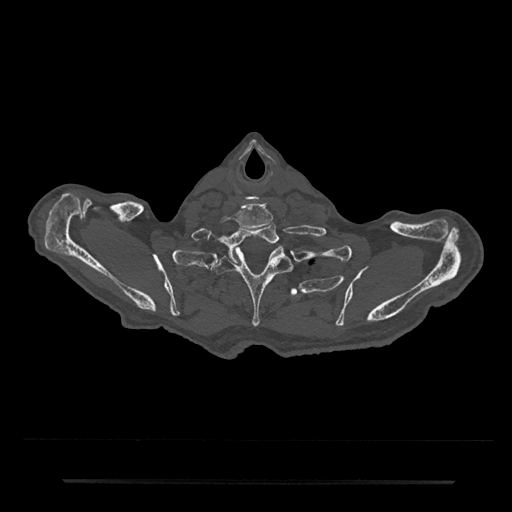
CT including the spine, one axial slice. Slice 706 of 797 in the series (ordered by position). 120 kVp. Bone window (W 1800 / L 400 HU). 512 × 512 image matrix, field of view 427 × 427 mm. Male patient, age 74 years. Case-level facts recorded for this patient, not image findings: primary cancer: prostate.
Annotated regions visible in this slice (semi-automatic segmentation, software-assisted and operator-edited):
- T1 vertebra: box from (x=221, y=222) to (x=279, y=265) px
- T2 vertebra: (x=211, y=248)–(x=292, y=328)
- T3 vertebra: (x=290, y=287)–(x=299, y=298)